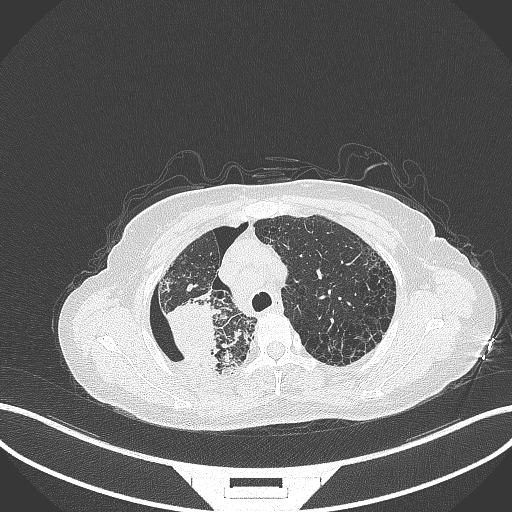
Chest CT, one axial slice; slice 274 of 408 in the series (ordered by position); reconstruction kernel B70f; lung window (W 1500 / L -600 HU); 1 mm slice thickness; 512 × 512 image matrix, field of view 400 × 400 mm. Female patient, age 64 years. From the clinical record (not read from this slice): clinical TNM (as recorded): T3 N3 M0.
Structures marked on this image (rectangle marked by the reading radiologist):
- lung tumour (recorded histology: squamous cell carcinoma): bounding box (x1, y1, x2, y2) in pixels: (160, 297, 224, 368)